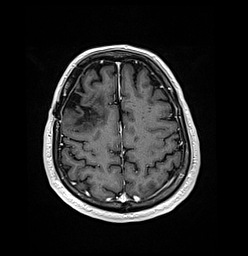
Brain MRI from a brain-tumour surgery series, one axial slice; slice 45 of 176 in the series (ordered by position); T1-weighted post-contrast; 1 mm slice thickness; 248 × 256 image matrix, field of view 242 × 250 mm. Case-level facts recorded for this patient, not image findings: histopathology: Oligodendroglioma; WHO grade: 3; IDH mutation: yes.
Outlined on this slice (outlined manually by an expert reader):
- previous resection cavity: bounding box [x1, y1, x2, y2] px = [64, 89, 89, 120]